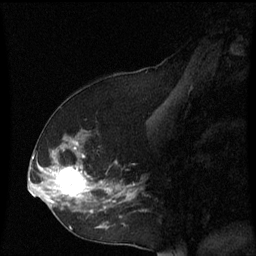
Breast MRI (dynamic contrast-enhanced), one sagittal slice; position 31 of 60 along the scan axis; dynamic contrast-enhanced series, image 2 of 3 at this slice position (ordered by acquisition); 1.5 T; TE 4.2 ms, TR 8.9 ms; 256 × 256 image matrix, field of view 200 × 200 mm. Patient: female, 53 years. From the clinical record (not read from this slice): setting: breast cancer imaged before/during neoadjuvant chemotherapy; receptor status: HR-positive, HER2-negative.
Annotated regions visible in this slice (semi-automatically segmented with operator editing):
- analysis volume of interest (the breast-tissue region the enhancement analysis was run in; not a lesion): bounding box <38,130,143,231> (left, top, right, bottom; pixels)
- tumour enhancement mask (voxels above the 70 % enhancement threshold inside the analysis volume of interest): <38,142,135,229>